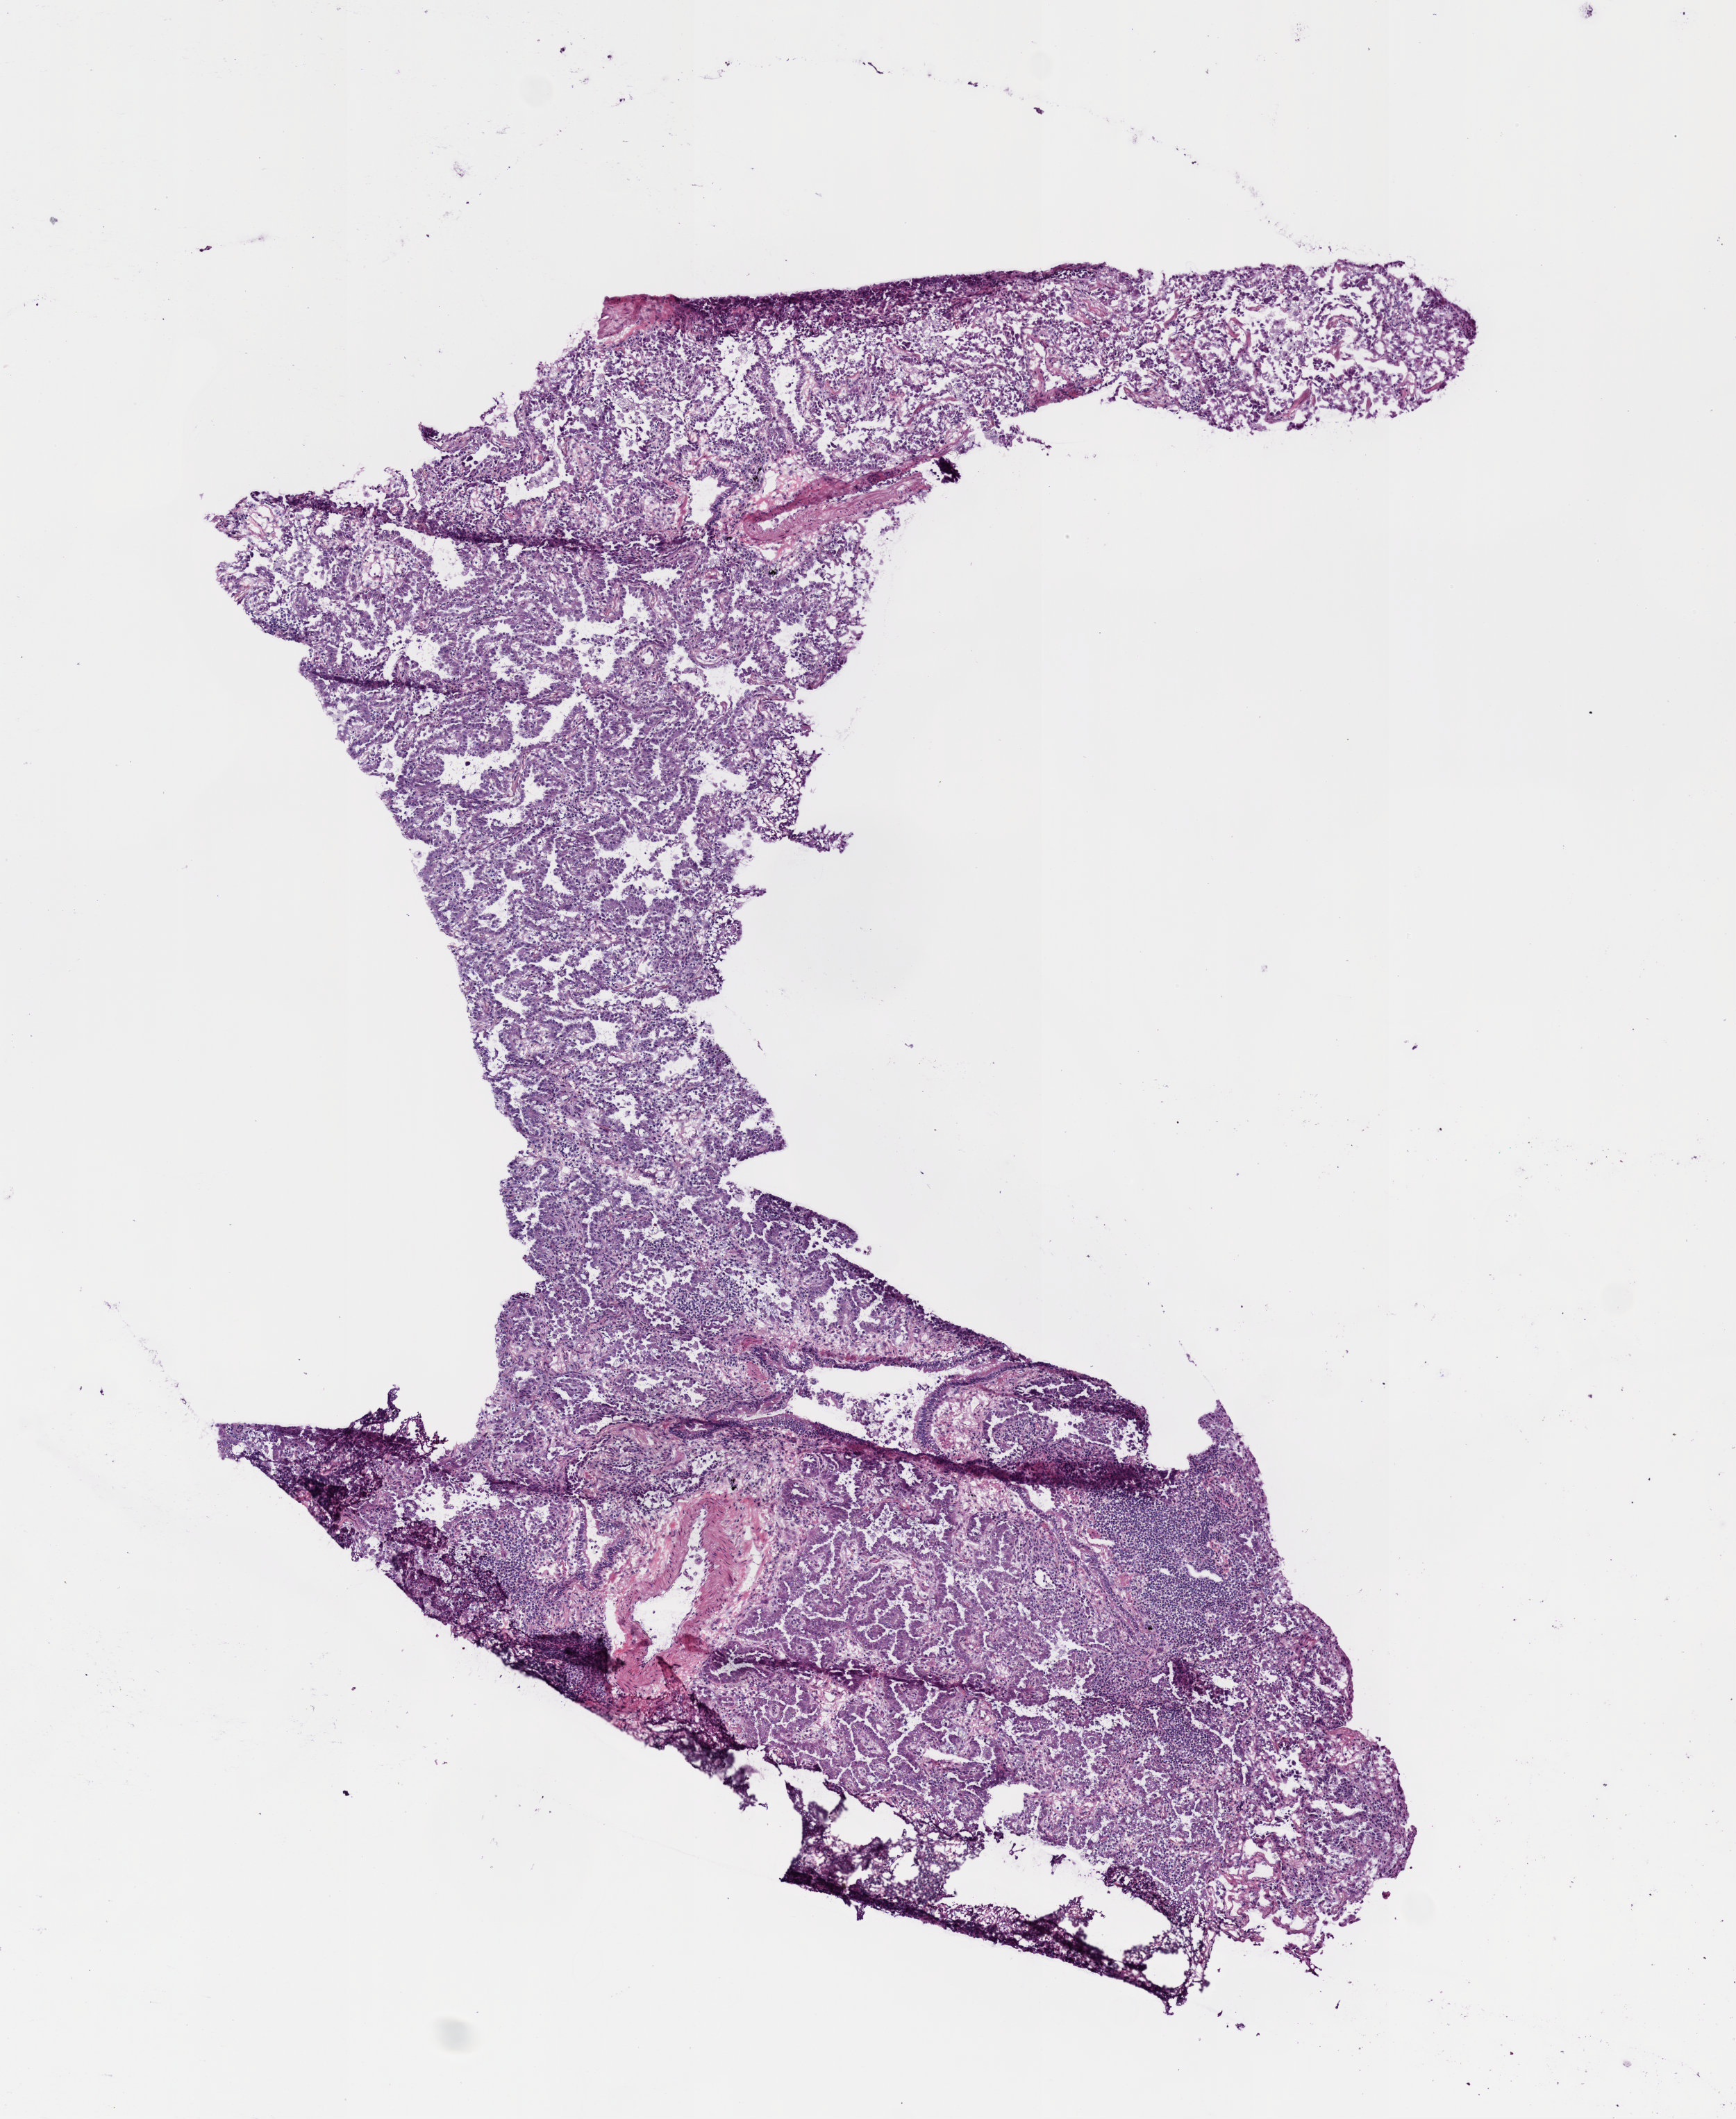
Hematoxylin and eosin (H&E) stained whole-slide image — a low-resolution overview of the entire scanned area, about 5.0 x 6.1 mm (from a 20x scan). Frozen section from the bottom of the tissue portion. Sample: primary tumour, lung. Female, age 73 years at initial diagnosis. Composition of this section per pathologist review: tumour cells 92%, tumour nuclei 75%, normal cells 3%, stromal cells 5%, necrosis 0%.
AJCC pathologic stage: IB (6th edition). Pathologic diagnosis: Adenocarcinoma, NOS (lower lobe, lung).